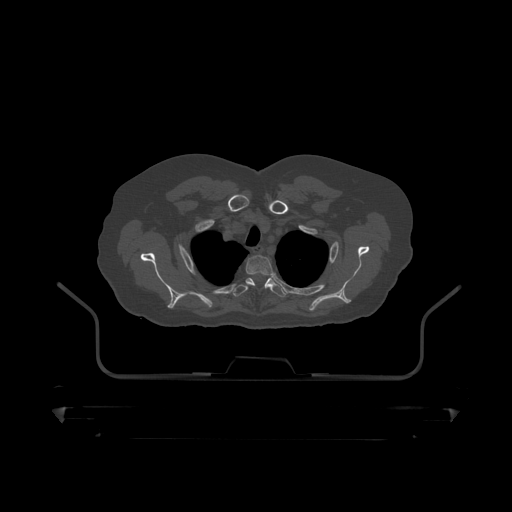
CT including the spine, one axial slice; reconstruction kernel STANDARD; bone window (W 1800 / L 400 HU); 512 × 512 image matrix, field of view 650 × 650 mm. Male patient, age 60 years. Case-level facts recorded for this patient, not image findings: primary cancer: prostate.
Outlined on this slice (semi-automatically segmented with operator editing):
- T2 vertebra: bounding box <246,256,276,278> (left, top, right, bottom; pixels)
- T3 vertebra: <233,278,286,297>